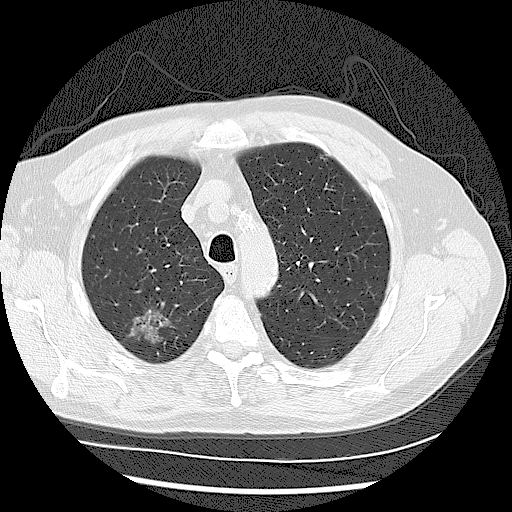
Low-dose screening chest CT, one axial slice. Position 91 of 122 along the scan axis. Lung window (W 1500 / L -600 HU). 512 × 512 image matrix, field of view 360 × 360 mm.
Outlined on this slice (manually delineated by an expert):
- lesion 1 (tumor, upper lobe of right lung): bounding box [x1, y1, x2, y2] px = [130, 309, 171, 342]